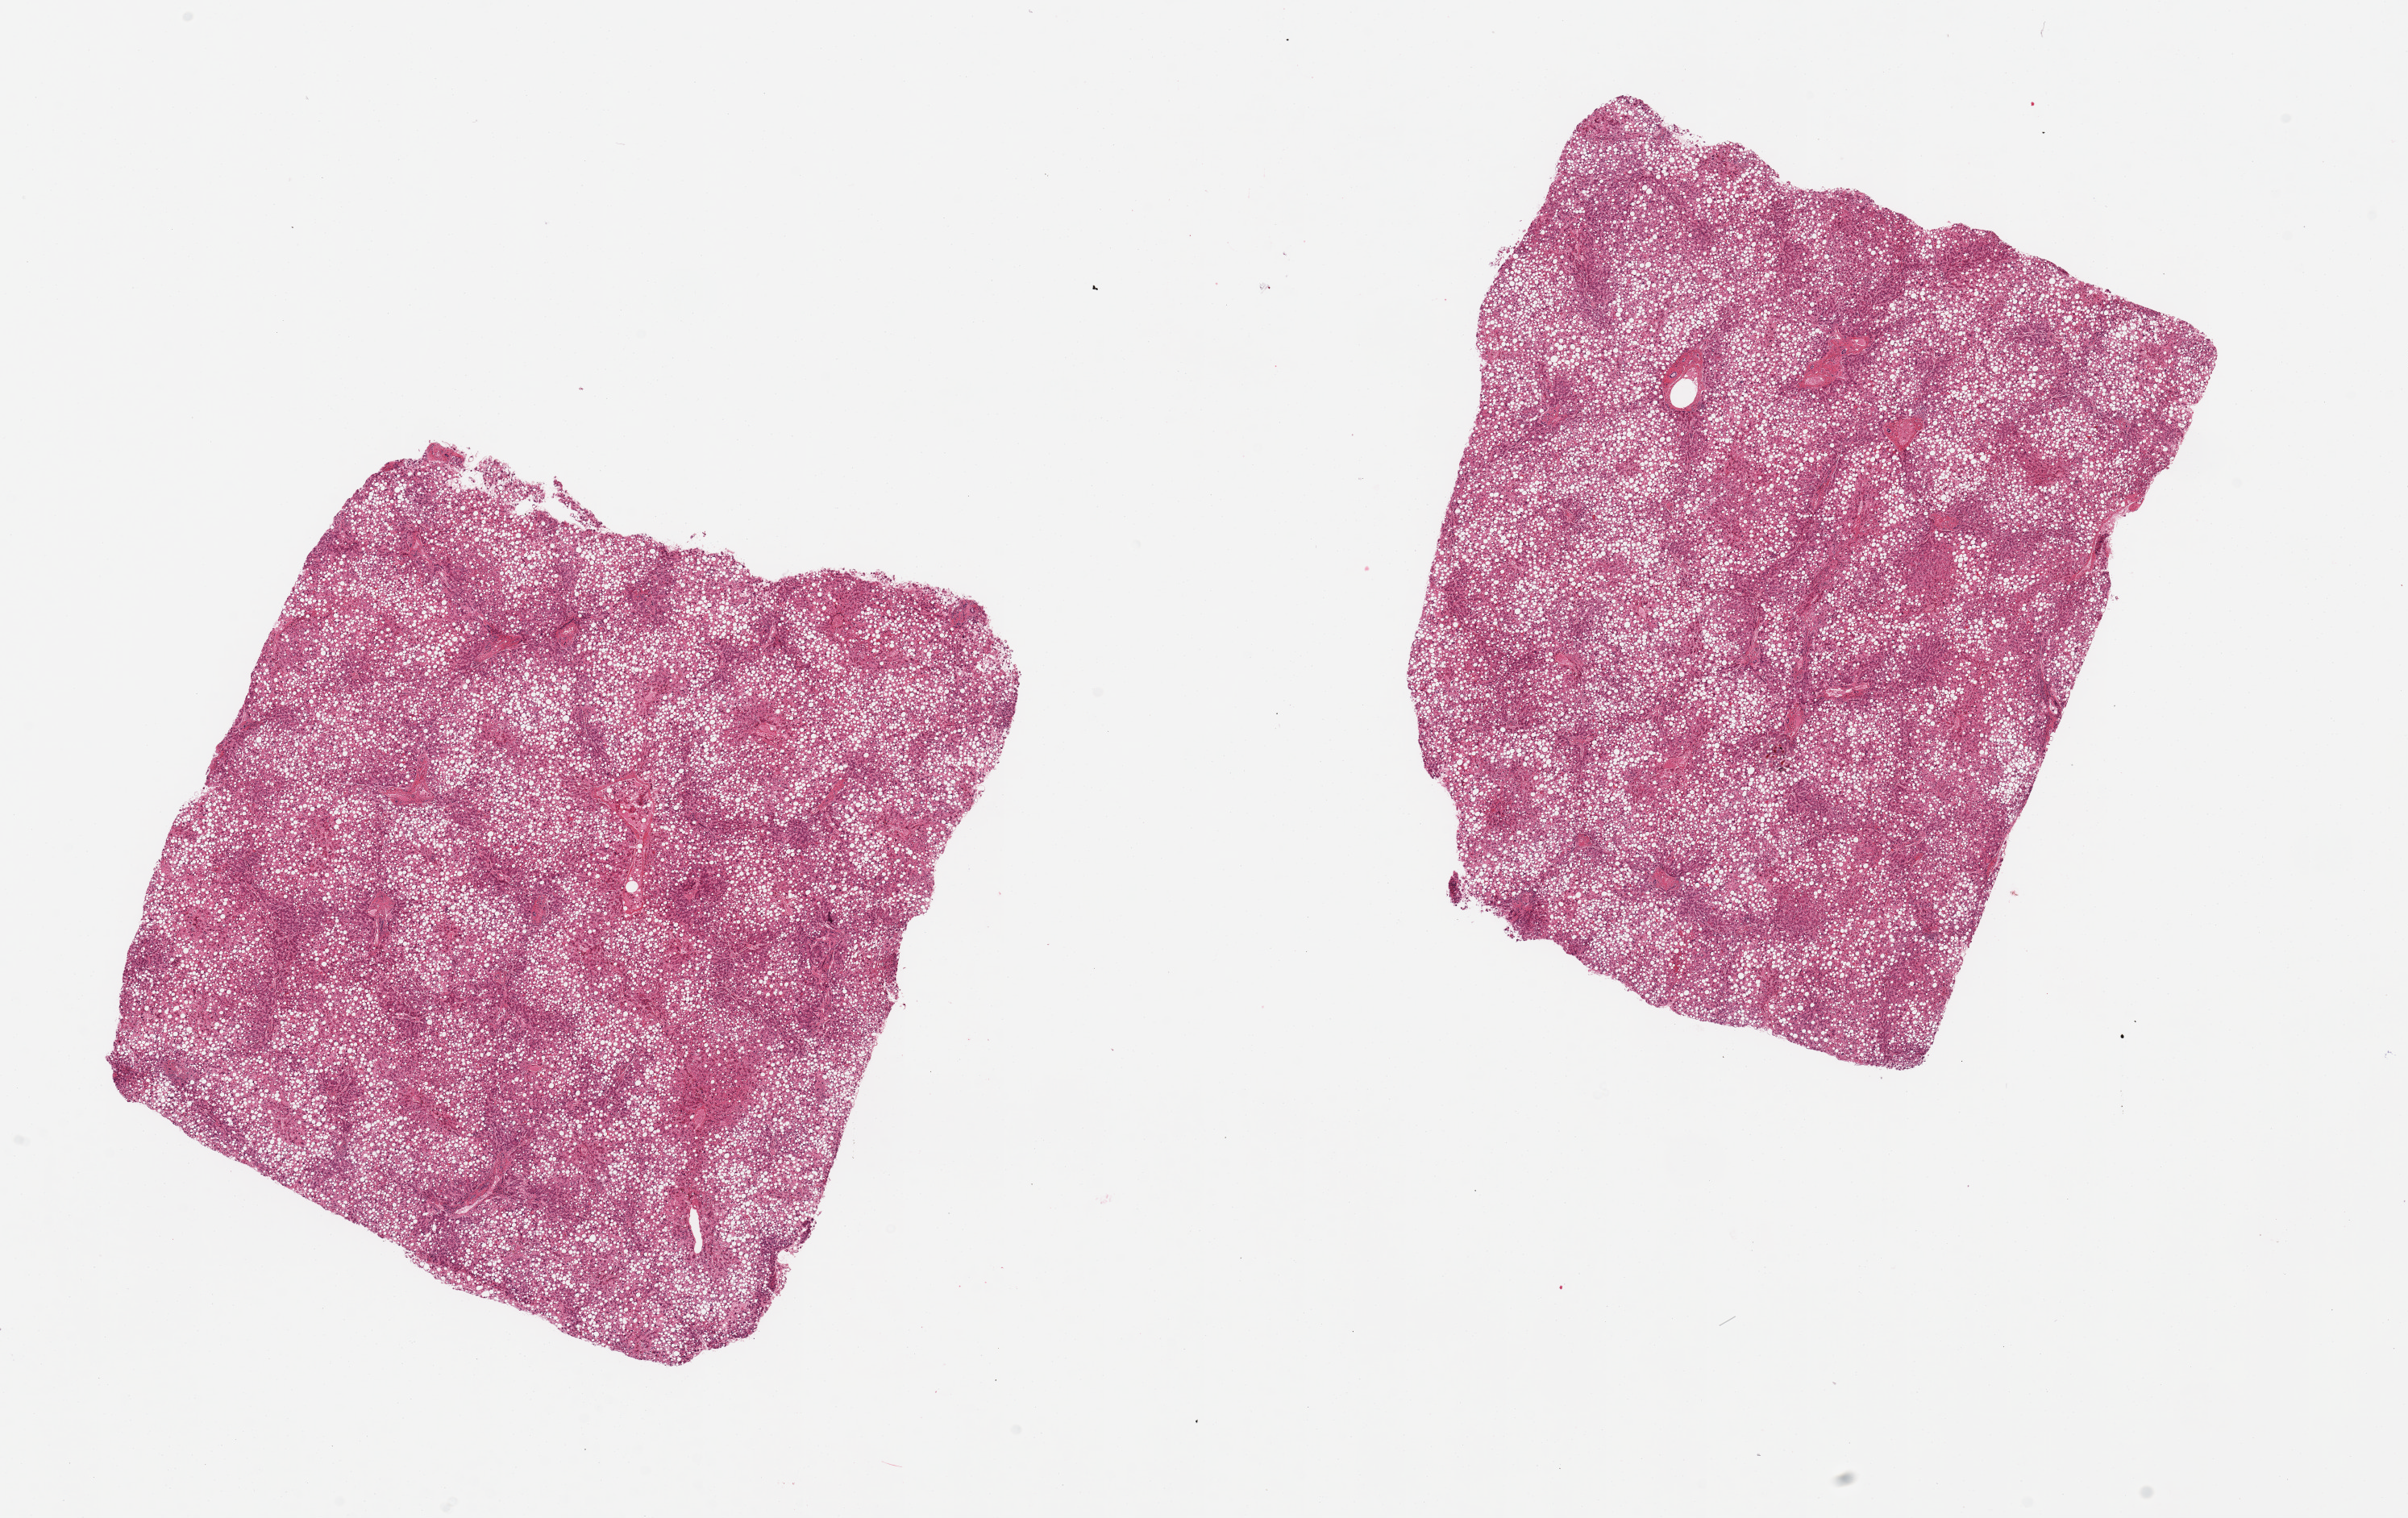
Digitized haematoxylin and eosin-stained section, brightfield, low-resolution overview of the scanned area, about 23.6 x 14.9 mm (from a 20x scan). PAXgene-fixed paraffin-embedded (PFPE) section. Target tissue: liver. Donor tissue sample. Male donor.
* pathologist's review note for this sample: 2 pieces, diffuse macrovesicular steatosis involves ~80% of parenchyma